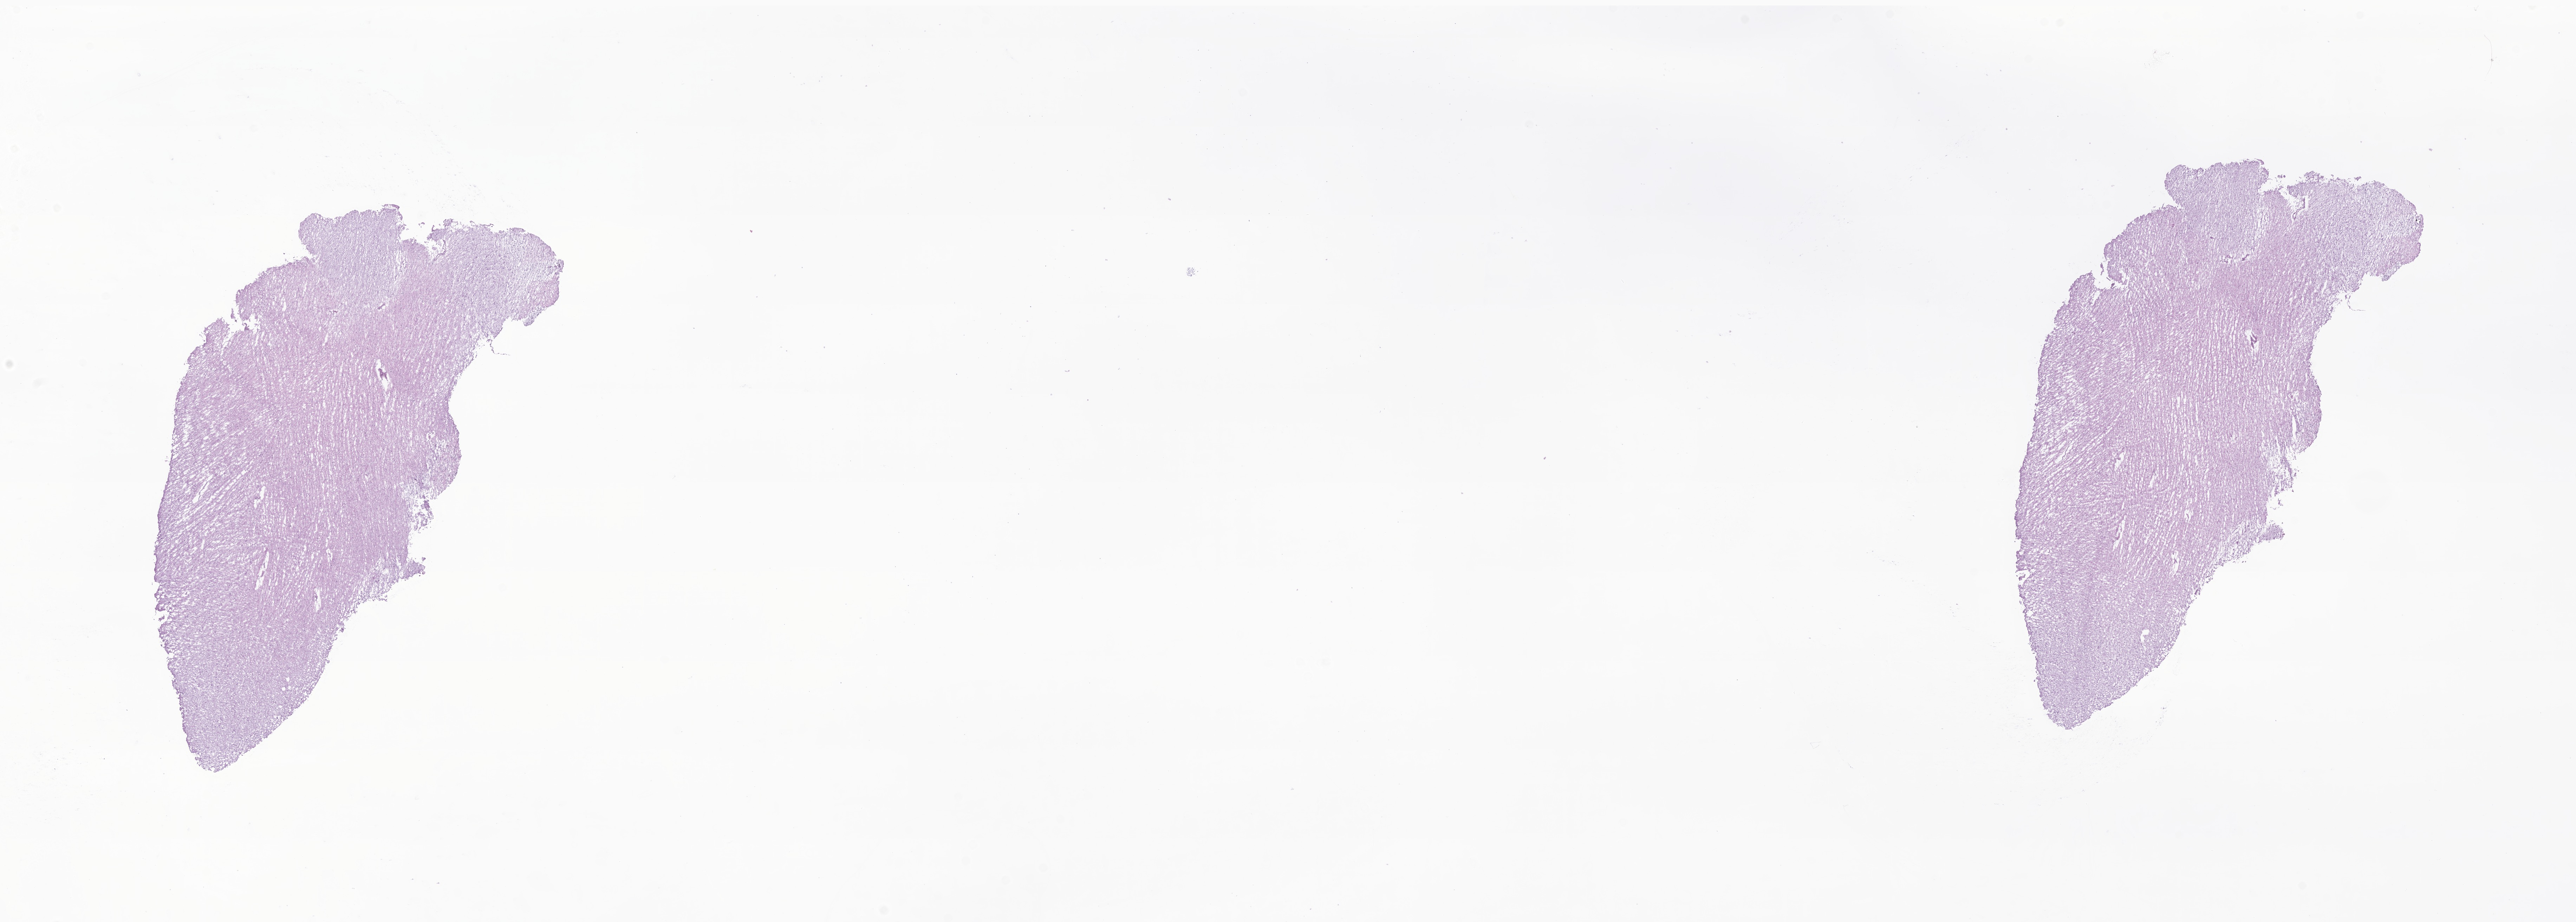
Hematoxylin and eosin (H&E) whole-slide image of tumor tissue from the brain — whole scanned area (about 30.9 x 11.1 mm) shown as a low-resolution overview, frozen section. Patient female; age 90 months.
* recorded diagnosis: Neoplasm, uncertain whether benign or malignant